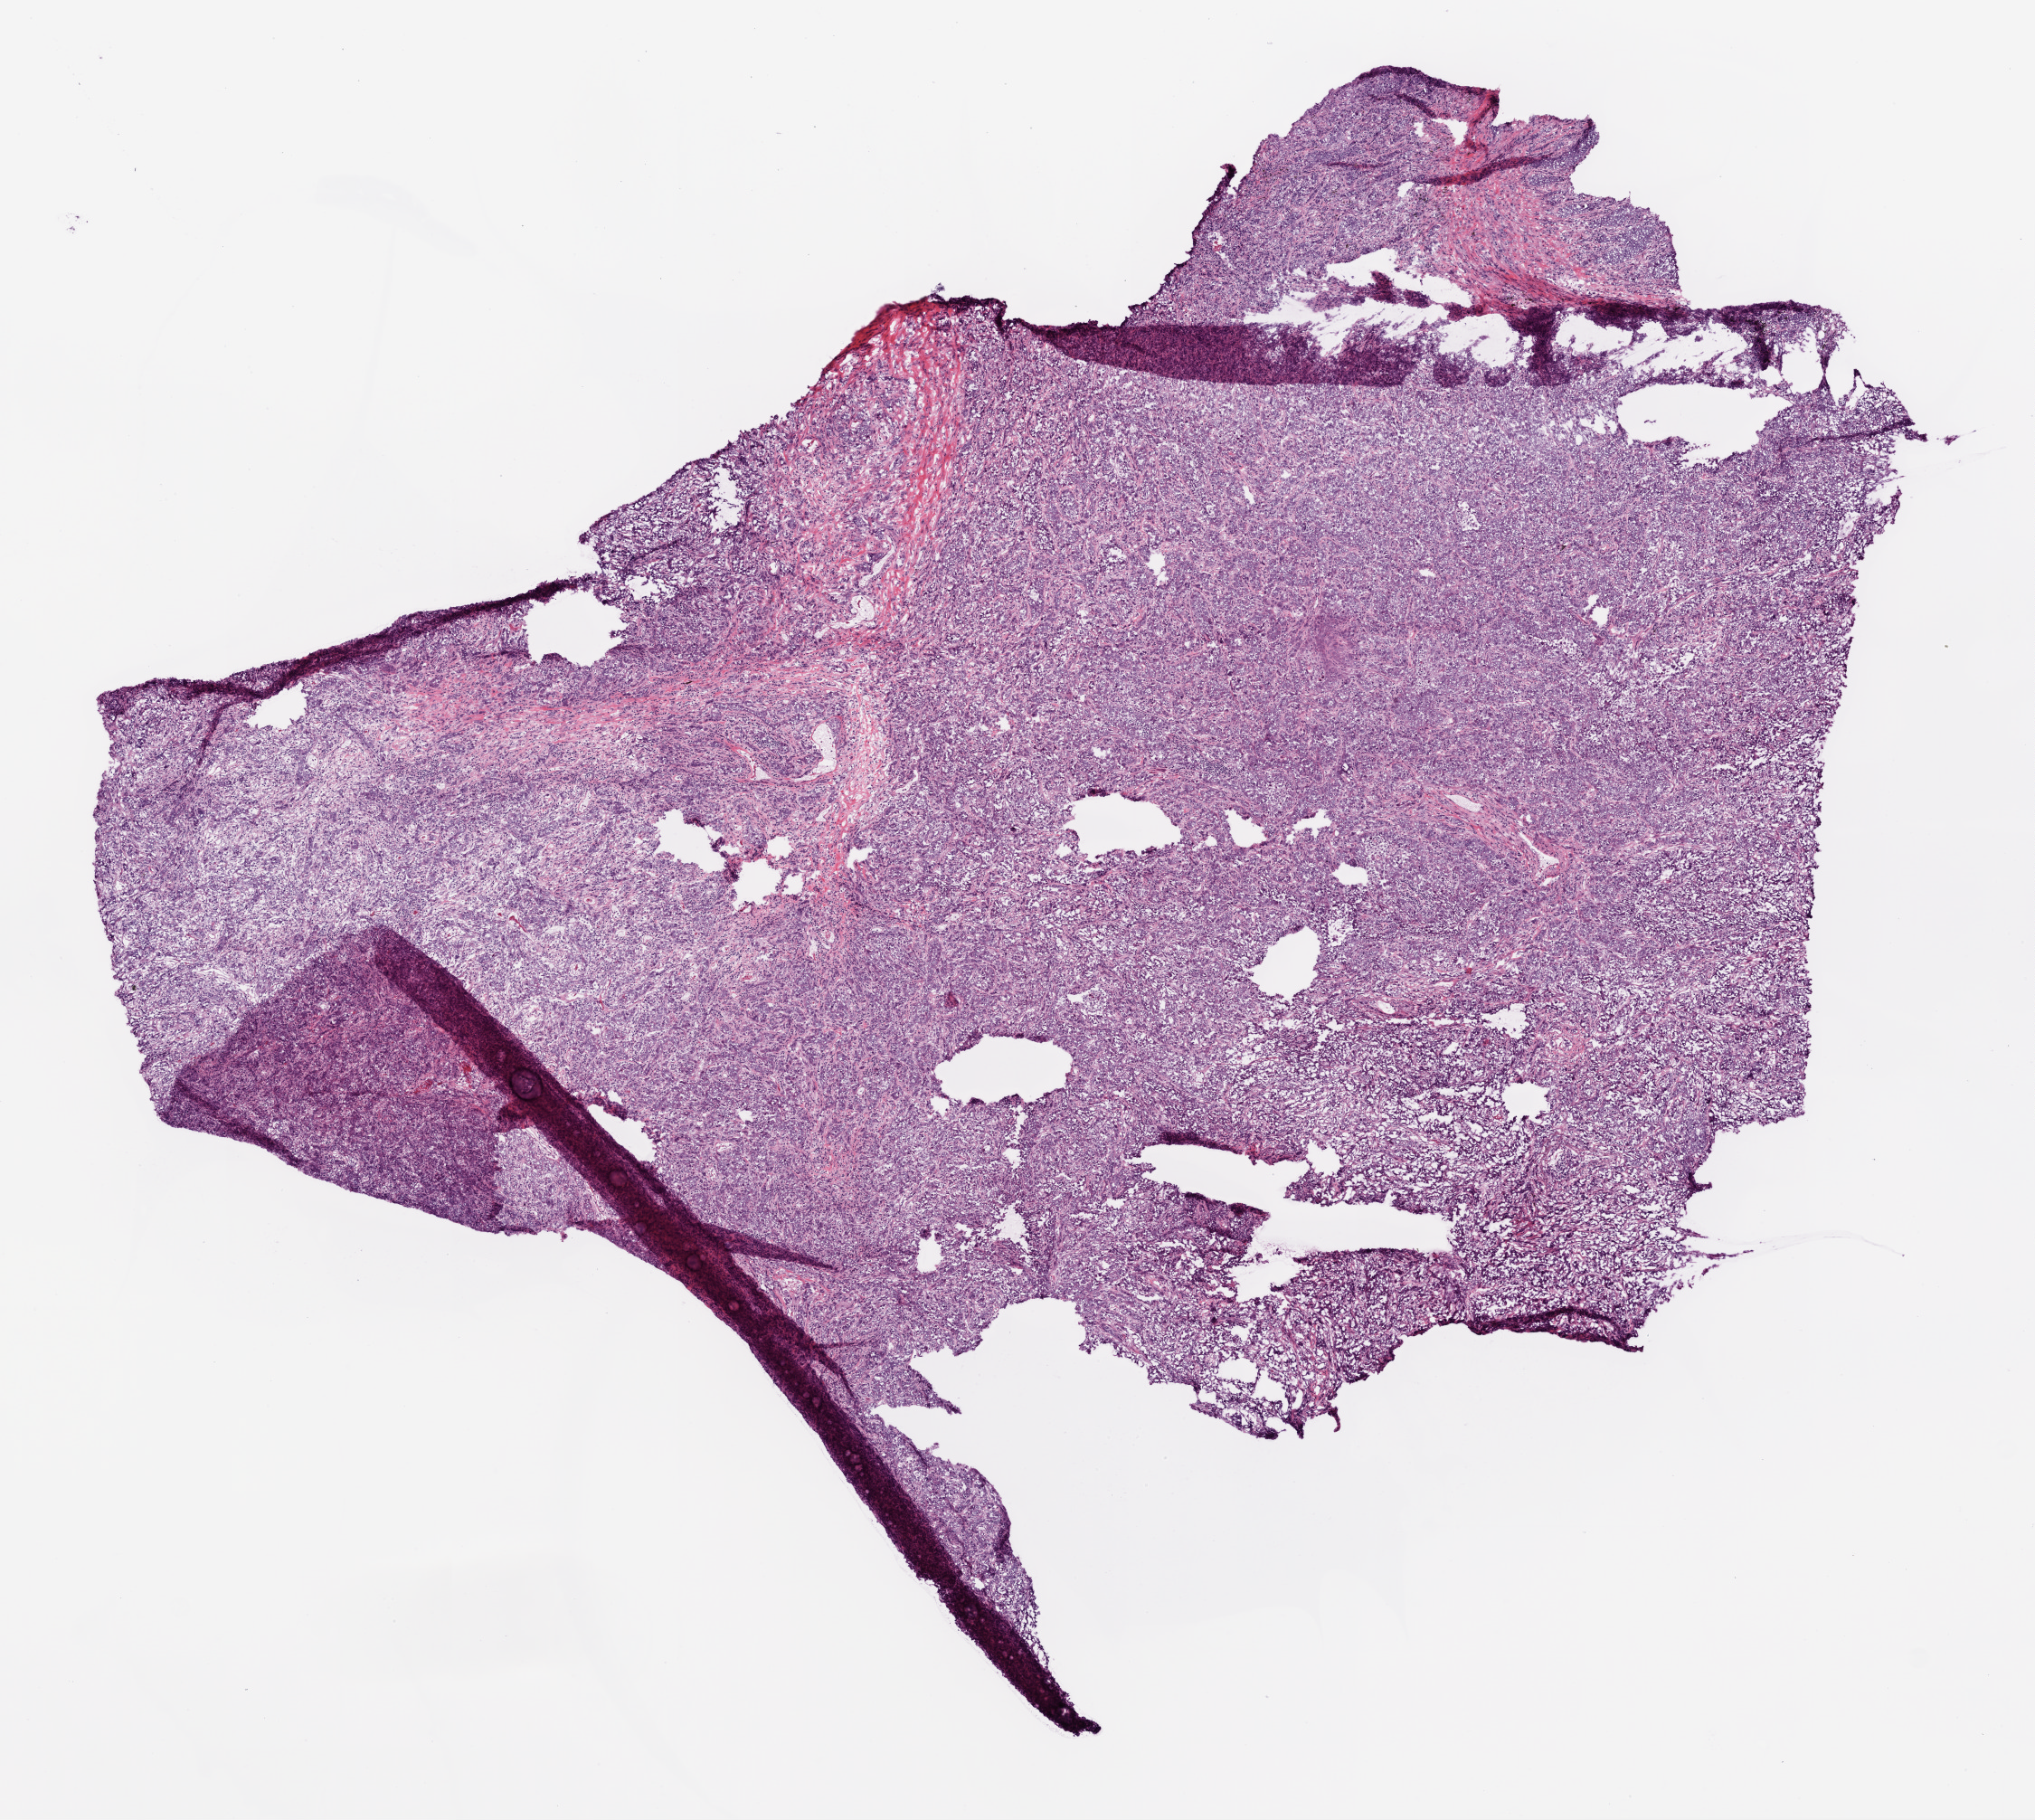
Whole-slide histology image, H&E — low-resolution overview of the scanned area, about 9.0 x 8.1 mm (from a 20x scan). Frozen section from the top of the tissue portion. Primary tumour sample from the lung. Male, age 57 years at initial diagnosis. Pathologist review of this section (percent, as recorded): tumour cells 87%, tumour nuclei 75%, normal cells 0%, stromal cells 10%, necrosis 3%.
Diagnosis: Squamous cell carcinoma, NOS.